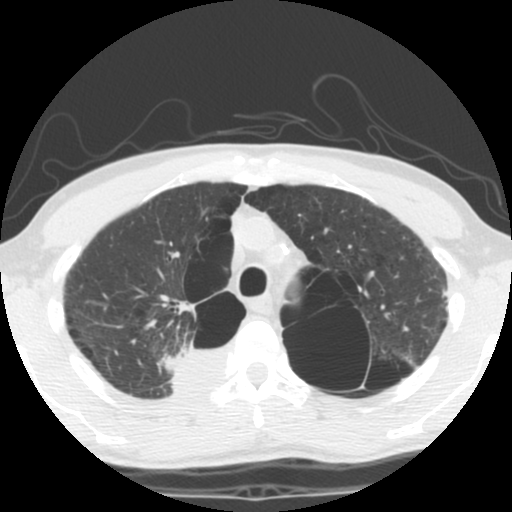
Chest CT (low-dose screening protocol), one axial image, second screening round (one year after baseline), lung window (W 1500 / L -600 HU), 2.5 mm slice thickness, standard (soft-tissue) reconstruction kernel (STANDARD), 140 kVp, slice 88 of 119 in the series. Male, age 62 years at enrolment. Current smoker at enrolment.
• Expert-annotated lung lesion, bounding box (x1, y1, x2, y2) in pixels: (129, 325, 225, 402).
• Screening reader's record for this exam (one nodule recorded; not confirmed to be the boxed lesion): non-calcified nodule or mass ≥4 mm, 35 × 25 mm, soft tissue attenuation.